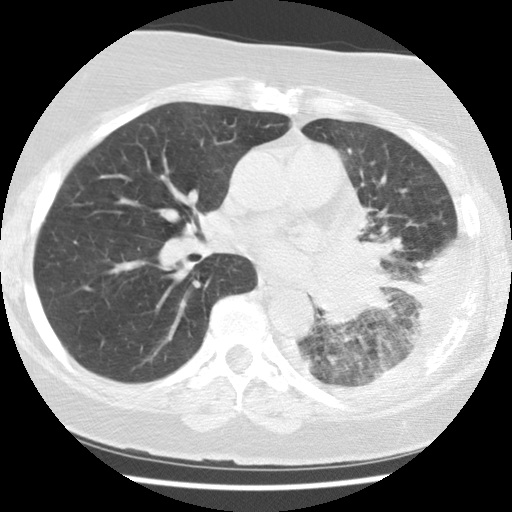
Axial slice from a low-dose chest CT screening exam; baseline screening round; lung window (W 1500 / L -600 HU); 2.5 mm slice thickness; 120 kVp; slice 57 of 114 in the series; 512 × 512 image matrix, field of view 320 × 320 mm. Female participant, aged 65 years at enrolment. Current smoker at enrolment.
- Expert-annotated lung lesion, bounding box (x1, y1, x2, y2) in pixels: (300, 282, 402, 363).
- Reader record for this screening exam (exam-level; its link to the box is not recorded): non-calcified nodule or mass ≥4 mm, left lower lobe, 74 × 48 mm, spiculated (stellate) margins, soft tissue attenuation.
- Later outcome: lung cancer diagnosed 13 days after this screen — adenocarcinoma, NOS, left lower lobe, stage IV (AJCC 6th edition), 74 mm at pathology.